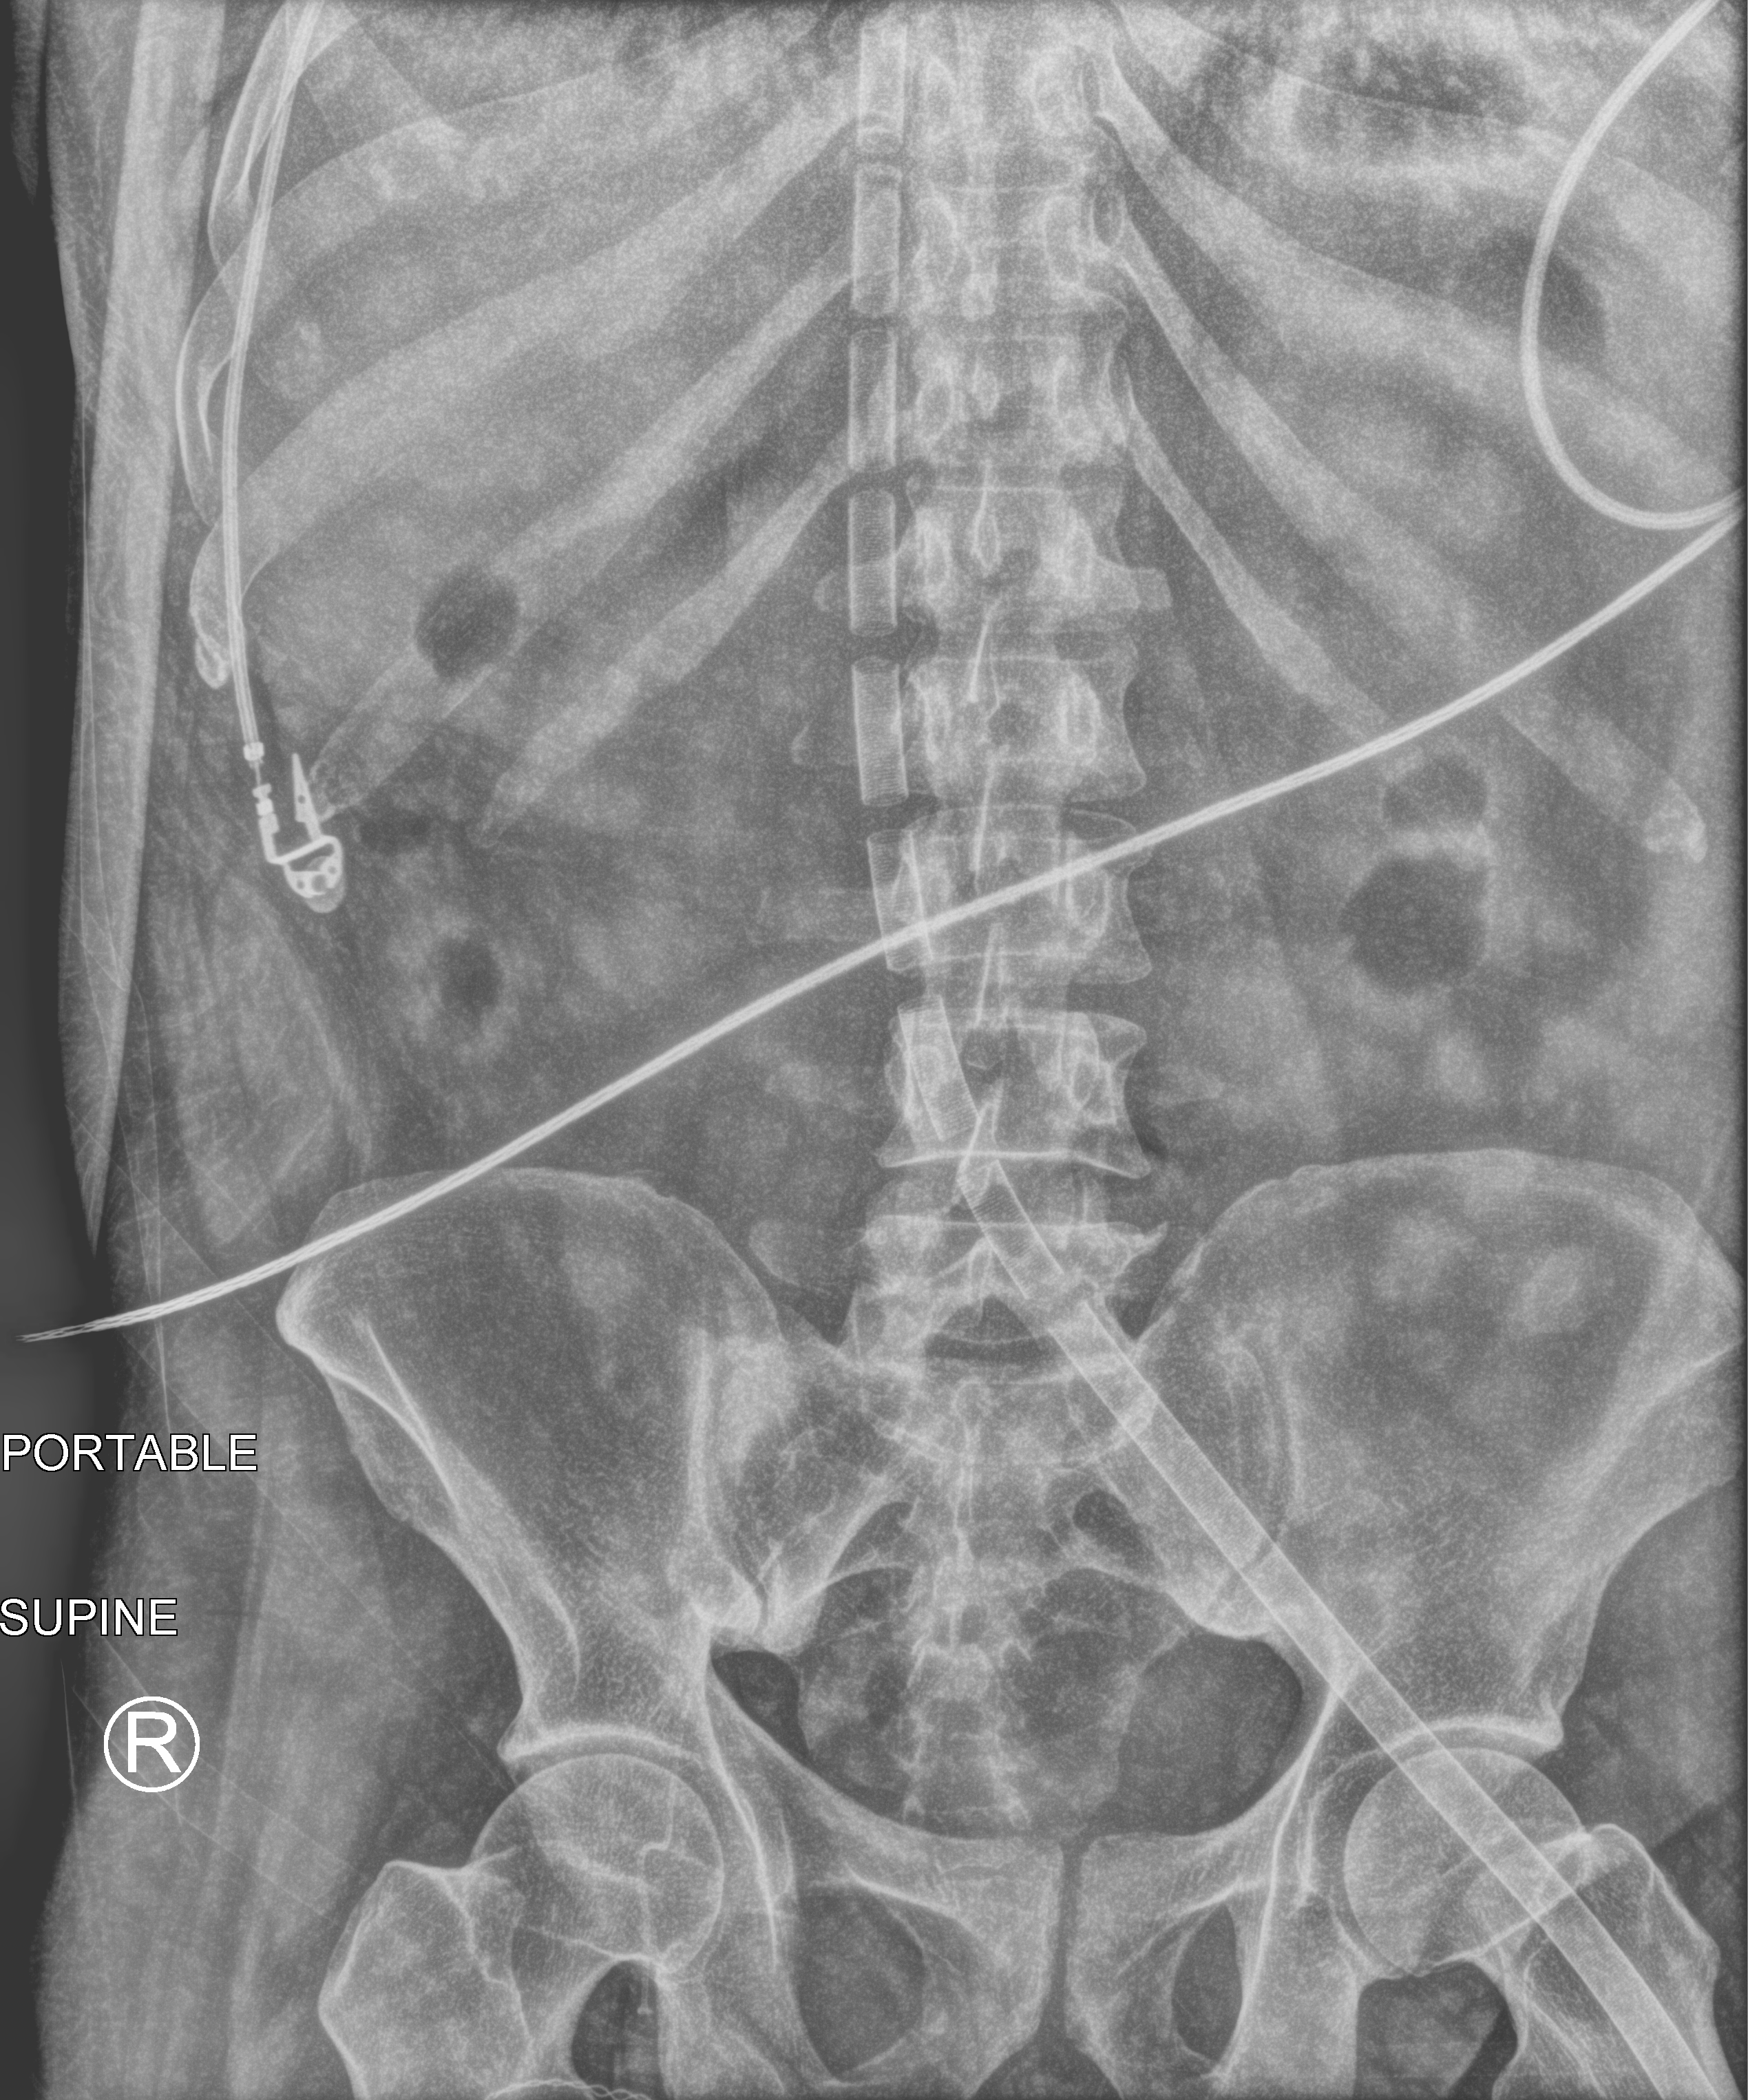
Portable abdomen radiograph, anteroposterior (AP) projection. Patient hospitalised with COVID-19; male, aged 18–59 years.
Admission-level facts for this patient (not findings on this image; timing relative to this image not recorded): admitted to intensive care during this hospital stay: yes; mechanically ventilated during this hospital stay: yes.